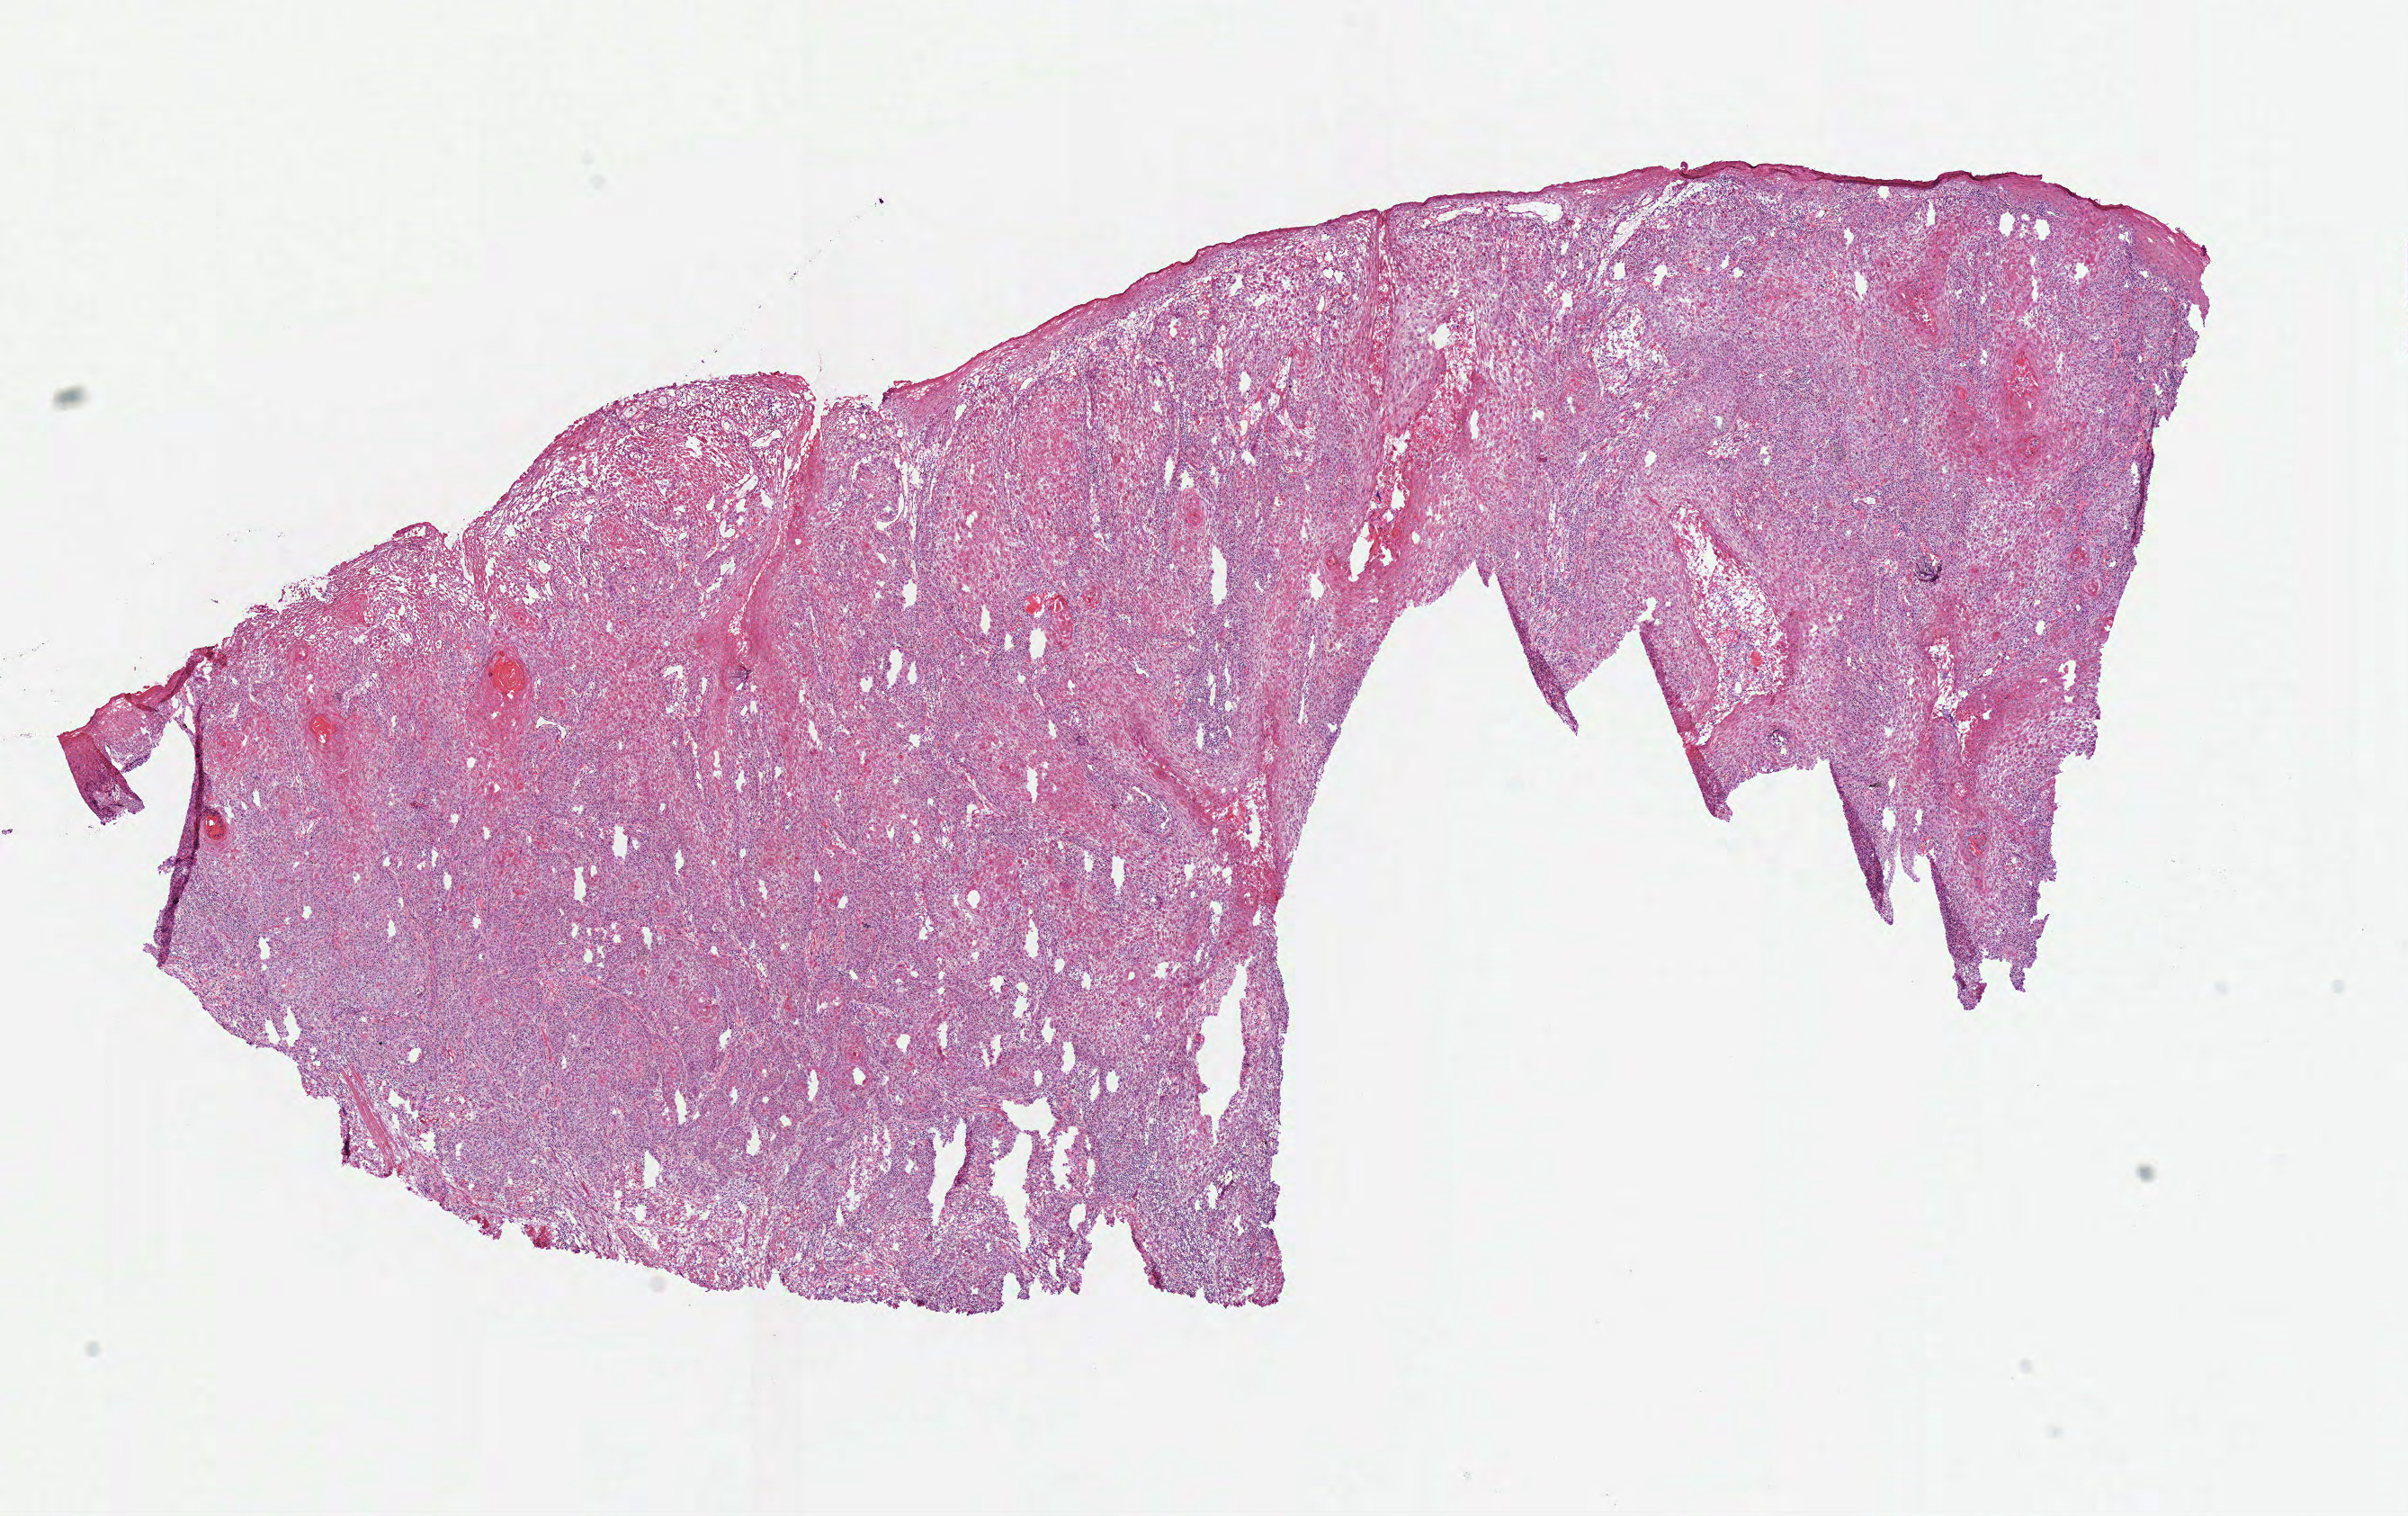
Whole-slide histology image, H&E, shown as a low-resolution overview of the whole scanned area (about 10.5 x 6.6 mm, slide scanned at 40x), frozen section, primary tumour sample from the head and neck. Male, age 73 years at initial diagnosis. Histologic grade: G2 (moderately differentiated). Slide review estimates, as recorded: tumour cells 89%, tumour nuclei 65%, normal cells 3%, stromal cells 5%, necrosis 3%.
- AJCC pathologic stage: I (7th edition)
- lymph nodes positive (case pathology): 0 of 9 examined
- histologic diagnosis: Squamous cell carcinoma, NOS
- laterality: right
- TNM: T1 N0